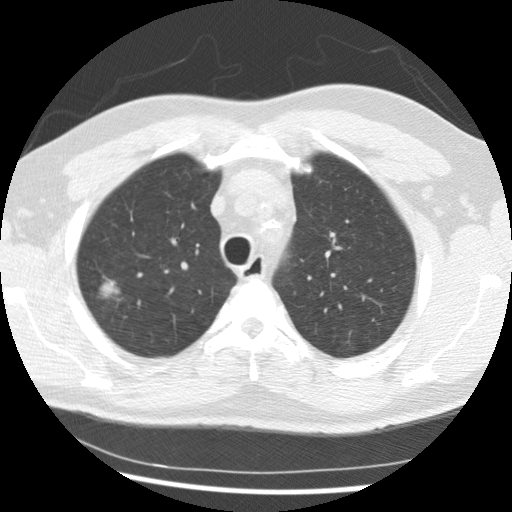
Chest CT (low-dose screening protocol), one axial image; baseline screening round; lung window (W 1500 / L -600 HU); 2.5 mm slice thickness; standard (soft-tissue) reconstruction kernel (STANDARD); slice 60 of 265 in the series; 512 × 512 image matrix, field of view 340 × 340 mm. Male, age 56 years at enrolment. Current smoker at enrolment.
- Lesion marked by an expert reader, bounding box [x1, y1, x2, y2] px = [77, 268, 131, 316].
- Screening reader's record for this exam (one nodule recorded; not confirmed to be the boxed lesion): non-calcified nodule or mass ≥4 mm, right upper lobe, 19 × 15 mm, spiculated (stellate) margins, soft tissue attenuation.
- Official screen result: positive, change unspecified: nodule(s) >= 4 mm or enlarging nodule(s), mass(es), or other non-specific abnormalities suspicious for lung cancer.